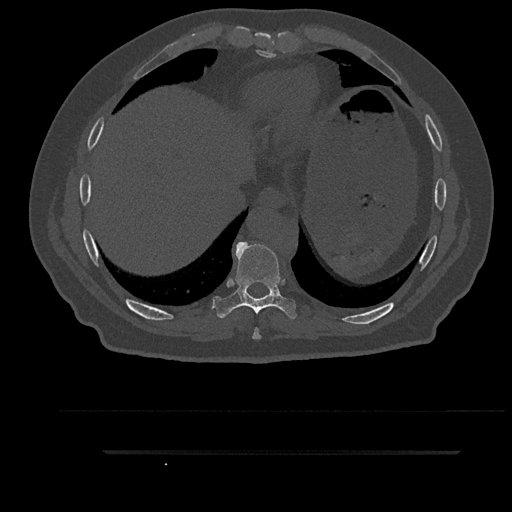
CT including the spine, one axial slice; slice 429 of 797 in the series (ordered by position); 120 kVp; bone window (W 1800 / L 400 HU); 0.5 mm slice thickness; 512 × 512 image matrix, field of view 432 × 432 mm. Male patient, age 63 years. Case-level facts recorded for this patient, not image findings: primary cancer: renal; vertebrae with lytic lesions (as recorded): T8.
Structures marked on this image (semi-automatically segmented with operator editing):
- T8 vertebra: box from (x=252, y=328) to (x=261, y=339) px
- T9 vertebra: (x=212, y=242)–(x=297, y=319)